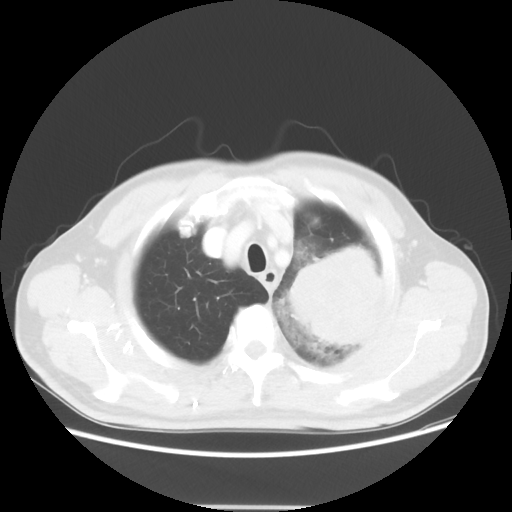
Chest CT, one axial slice. Slice 47 of 53 in the series (ordered by position). 100 kVp. Lung window (W 1500 / L -600 HU). 5 mm slice thickness. 512 × 512 image matrix, field of view 391 × 391 mm. Patient: male, 60 years. From the clinical record (not read from this slice): clinical TNM (as recorded): T4 N1 M1a.
Annotated regions visible in this slice (bounding box drawn by a radiologist):
- lung tumour (recorded histology: large cell carcinoma): bounding box <278,245,389,356> (left, top, right, bottom; pixels)